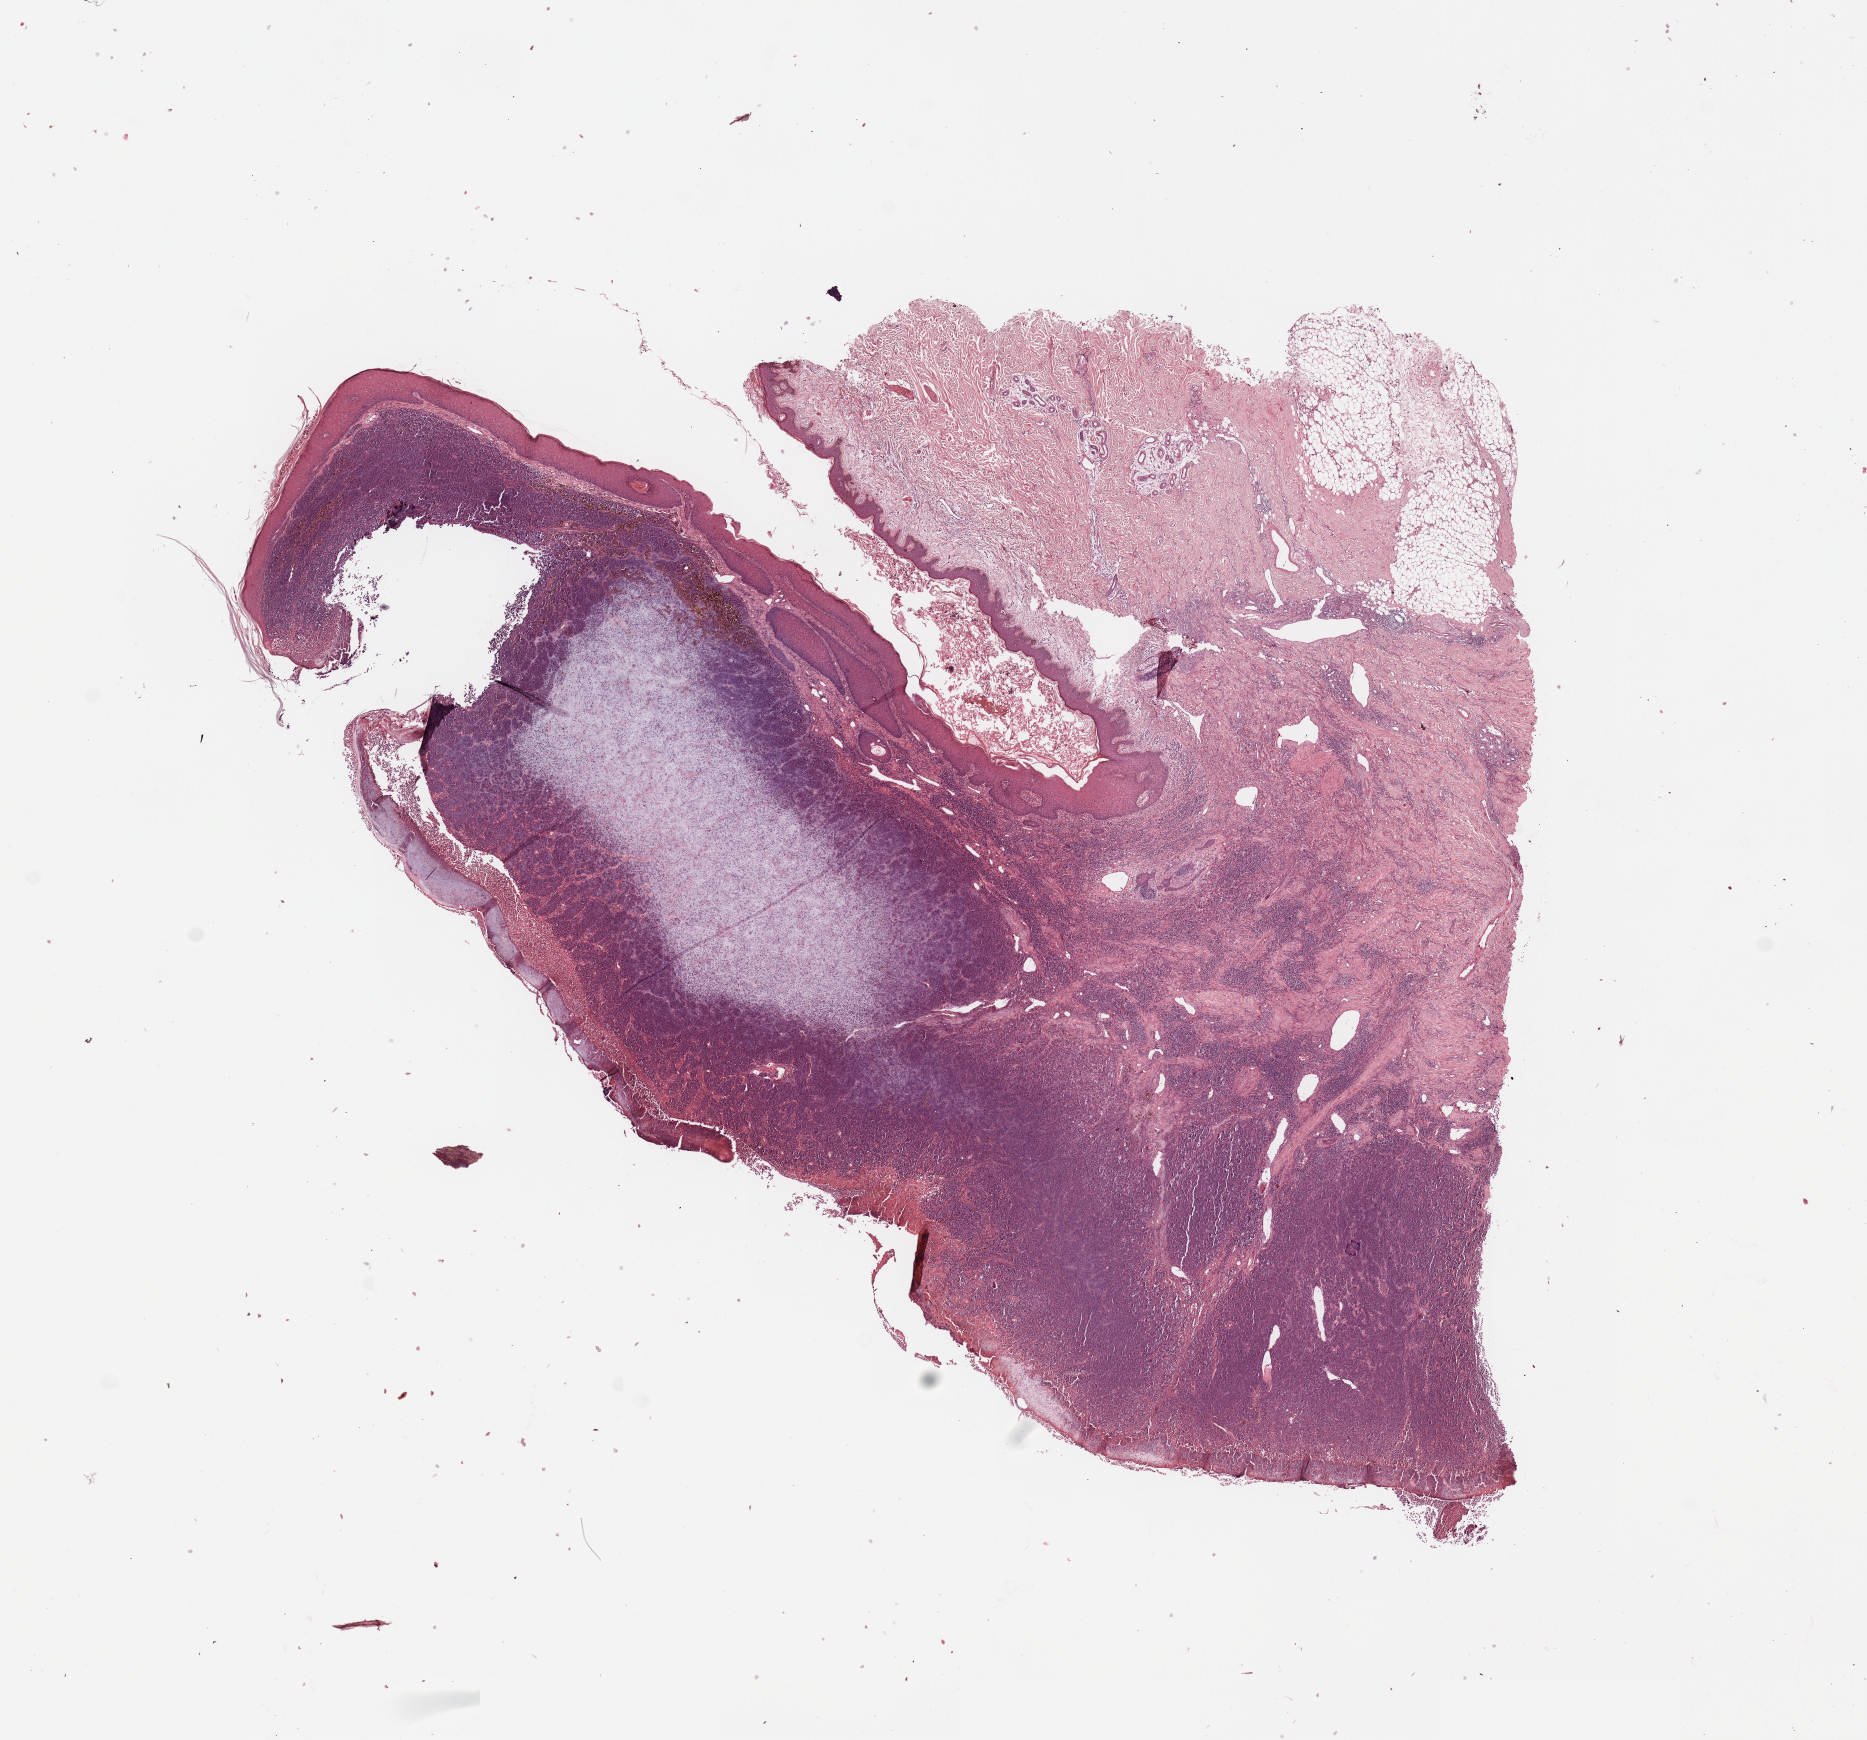
H&E-stained whole-slide image, whole scanned area (about 14.8 x 13.8 mm) shown as a low-resolution overview, melanoma tumour tissue; sampled site not recorded. Male, 59 y/o.
Histologic diagnosis: Malignant melanoma, NOS. Primary tumour site (as recorded): extremities. AJCC pathologic stage: IIC.